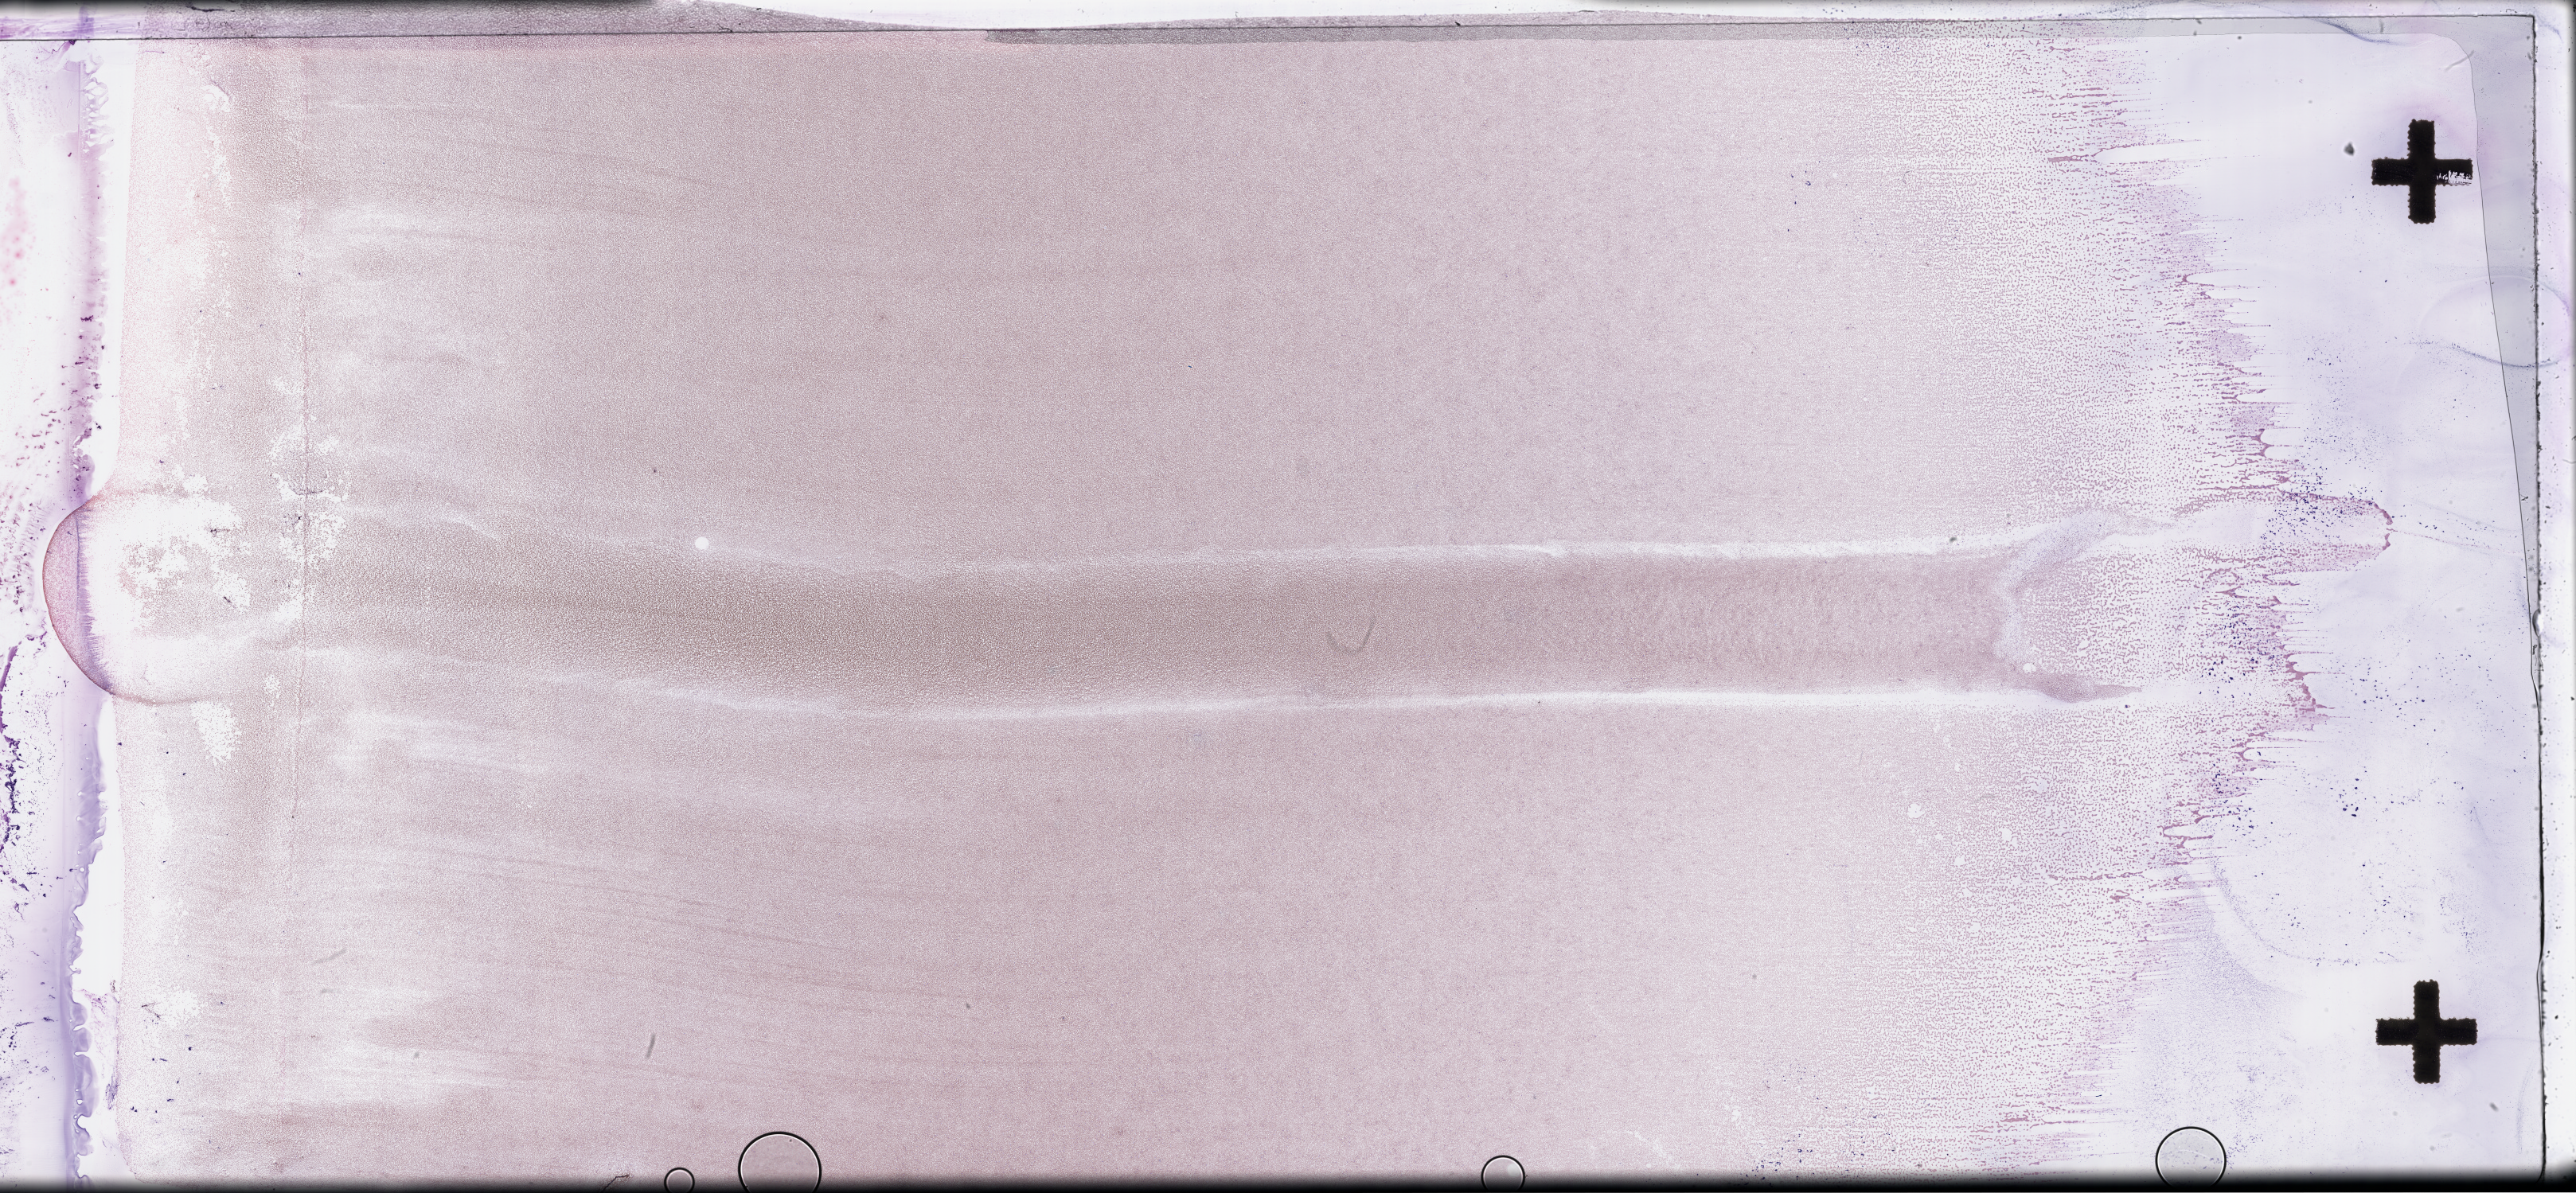
Wright-Giemsa-stained whole blood smear, whole-slide image, a low-resolution overview of the entire scanned area, about 52.3 x 24.2 mm; EDTA-anticoagulated smear; specimen time point: collected on treatment. Male patient.
* from a patient with: Plasma Cell Myeloma